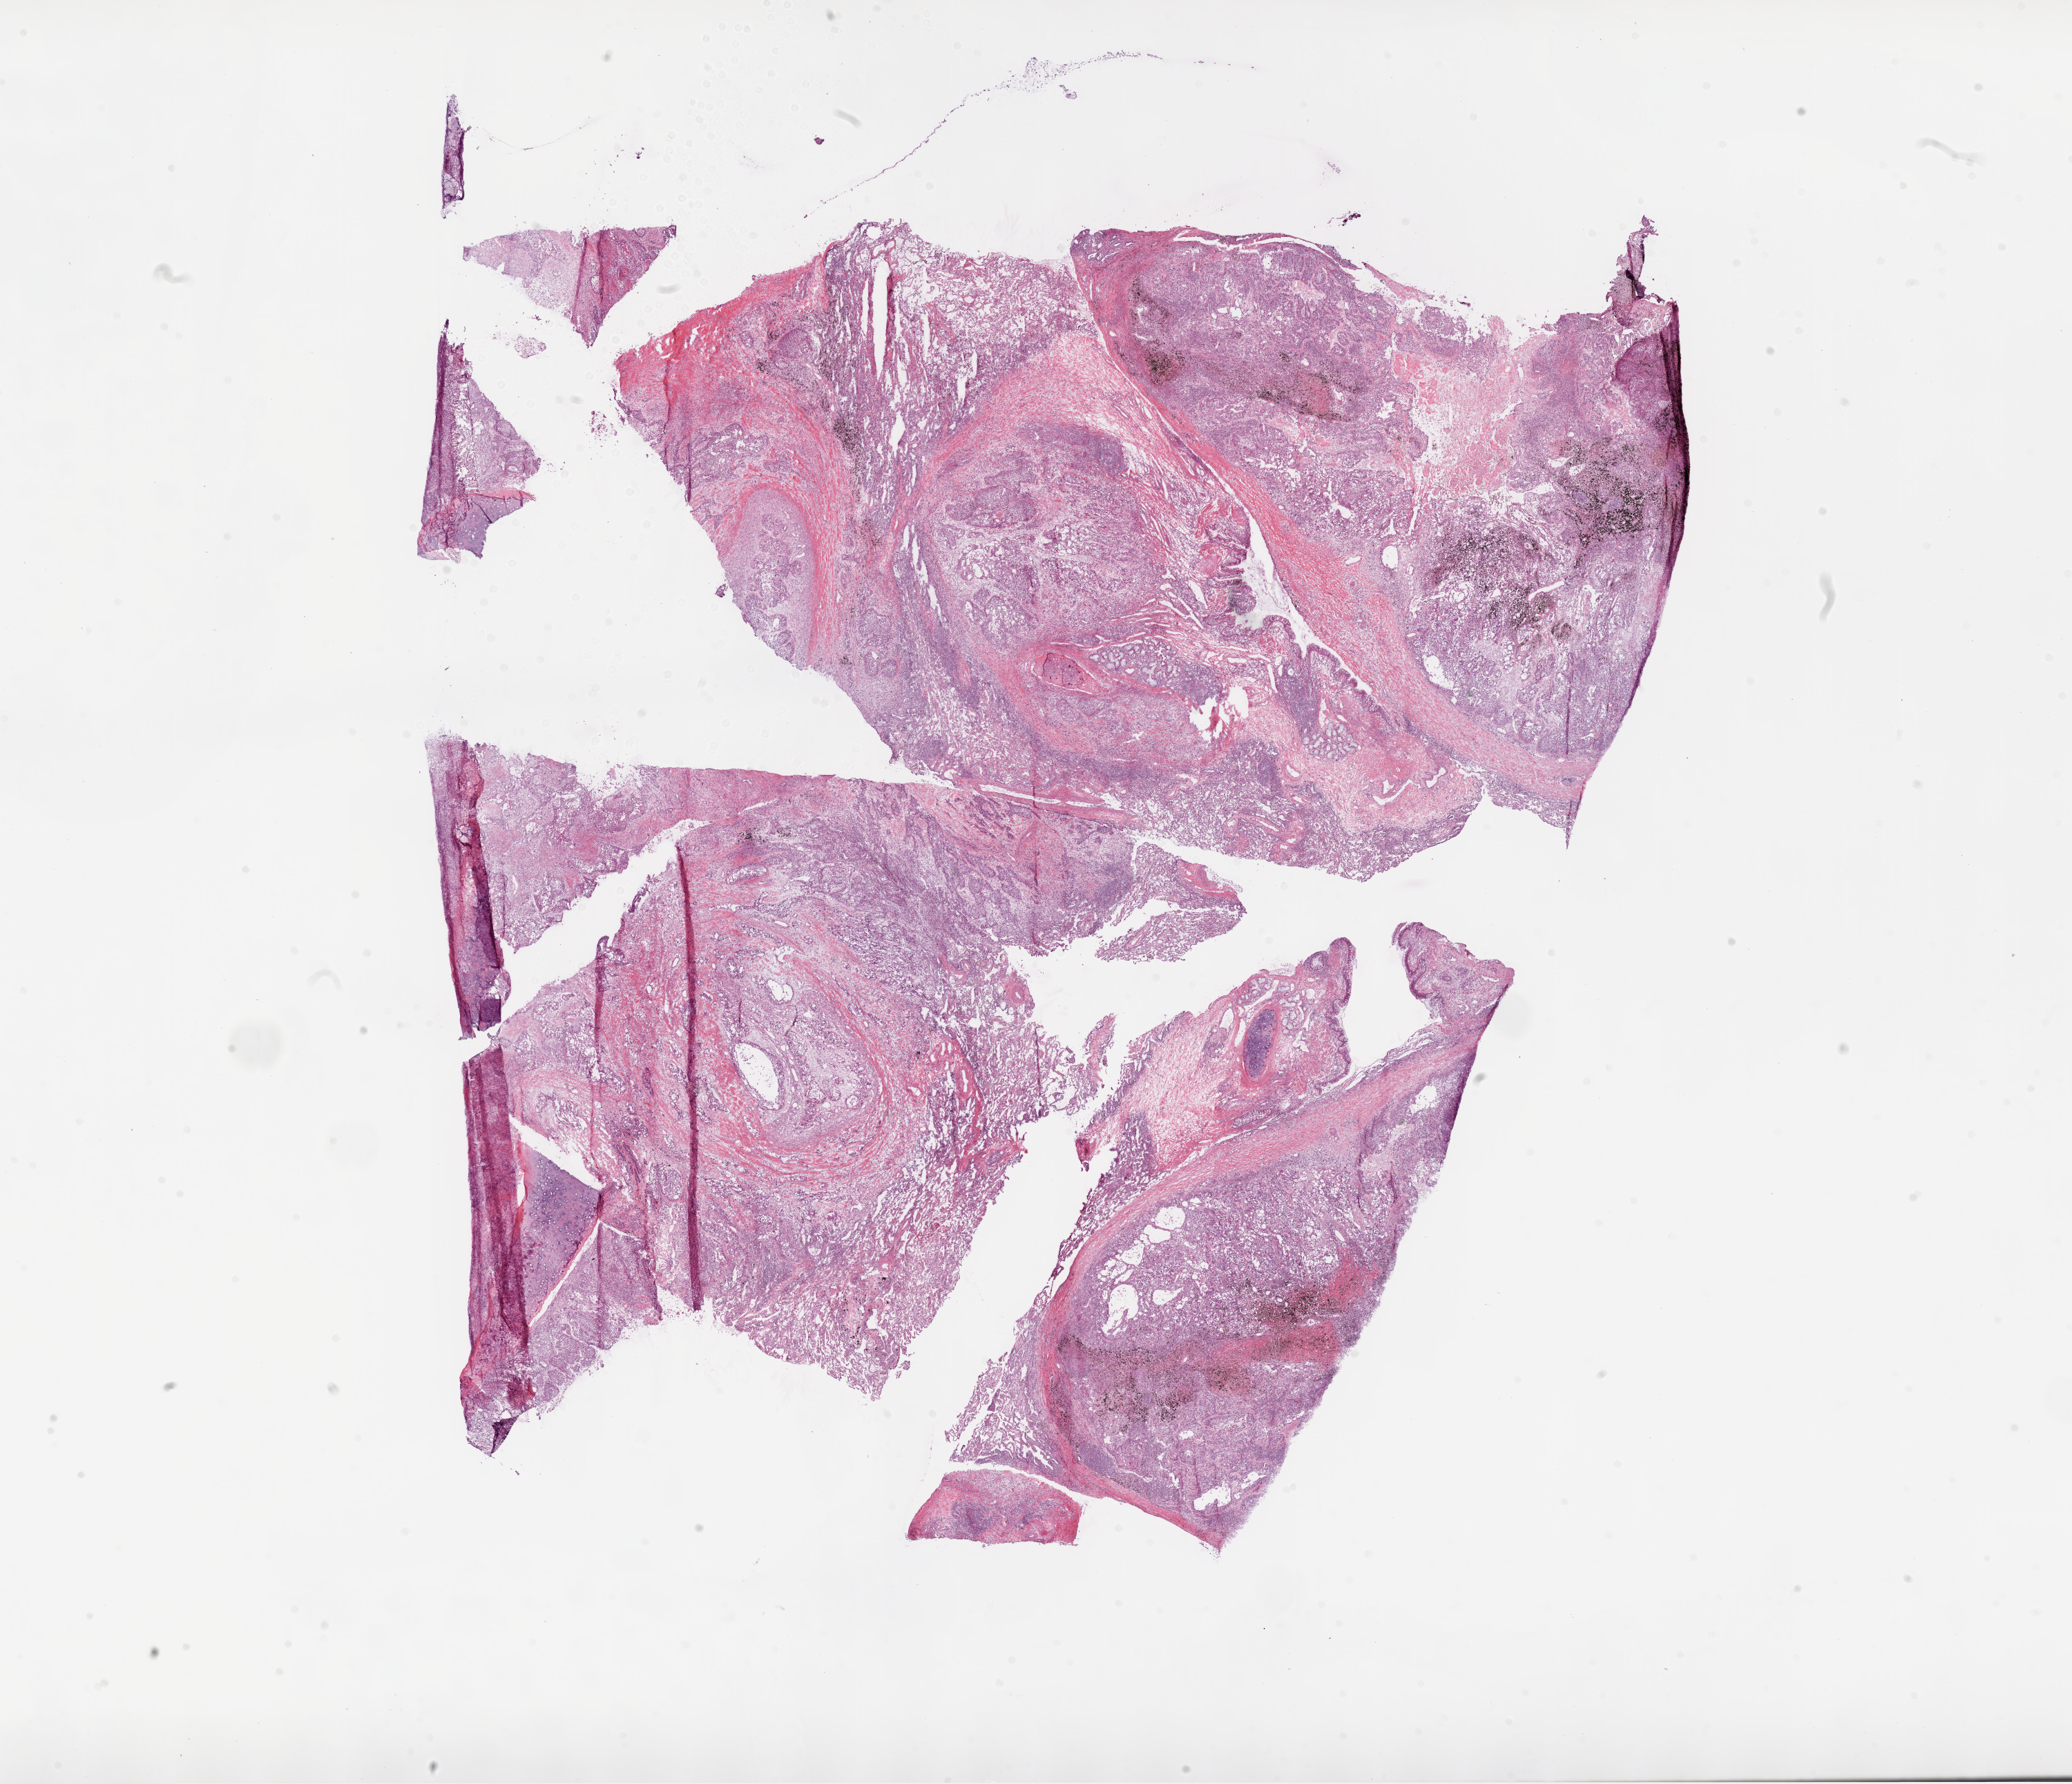
Digitized Hematoxylin and eosin (H&E) stained tissue section (whole slide) — low-resolution overview of the scanned area, about 24.1 x 20.7 mm (acquisition: 20x scan); frozen section; sample: primary tumour, lung. Male, age 67 years at initial diagnosis. Slide review estimates, as recorded: tumour cells 57%, tumour nuclei 70%.
Histologic diagnosis: Squamous cell carcinoma, NOS (lower lobe, lung).